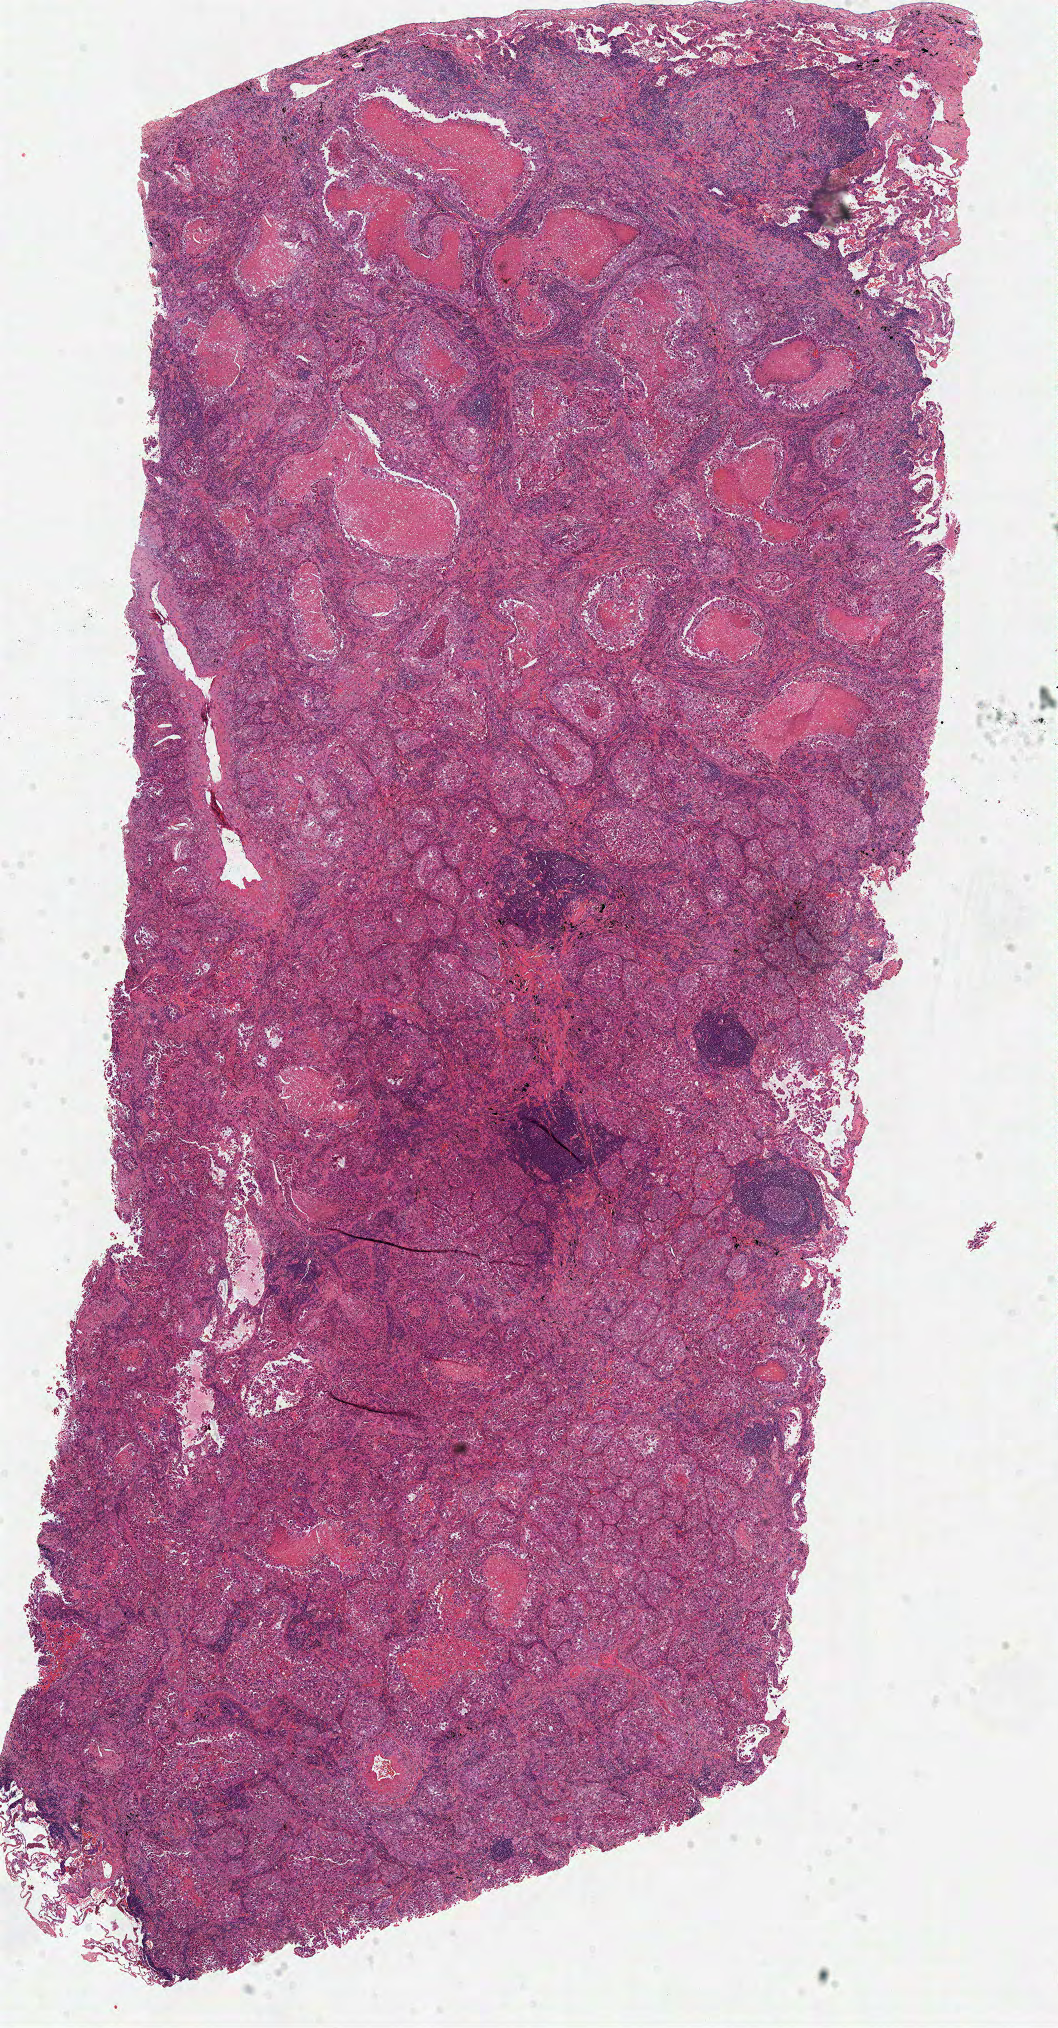
Hematoxylin and eosin (H&E) stained whole-slide image — a low-resolution overview of the entire scanned area, about 8.3 x 15.9 mm, frozen section from the top of the tissue portion, sample: primary tumour, lung. Female, age 85 years at initial diagnosis. Composition of this section per pathologist review: tumour cells 75%, tumour nuclei 61%, normal cells 5%, stromal cells 0%, necrosis 20%. Inflammatory infiltration, as recorded: lymphocyte infiltration 30%, monocyte infiltration 0%, neutrophil infiltration 0%.
• laterality: left
• pathologic diagnosis: Adenocarcinoma, NOS (upper lobe, lung)
• AJCC pathologic stage: IB (6th edition)